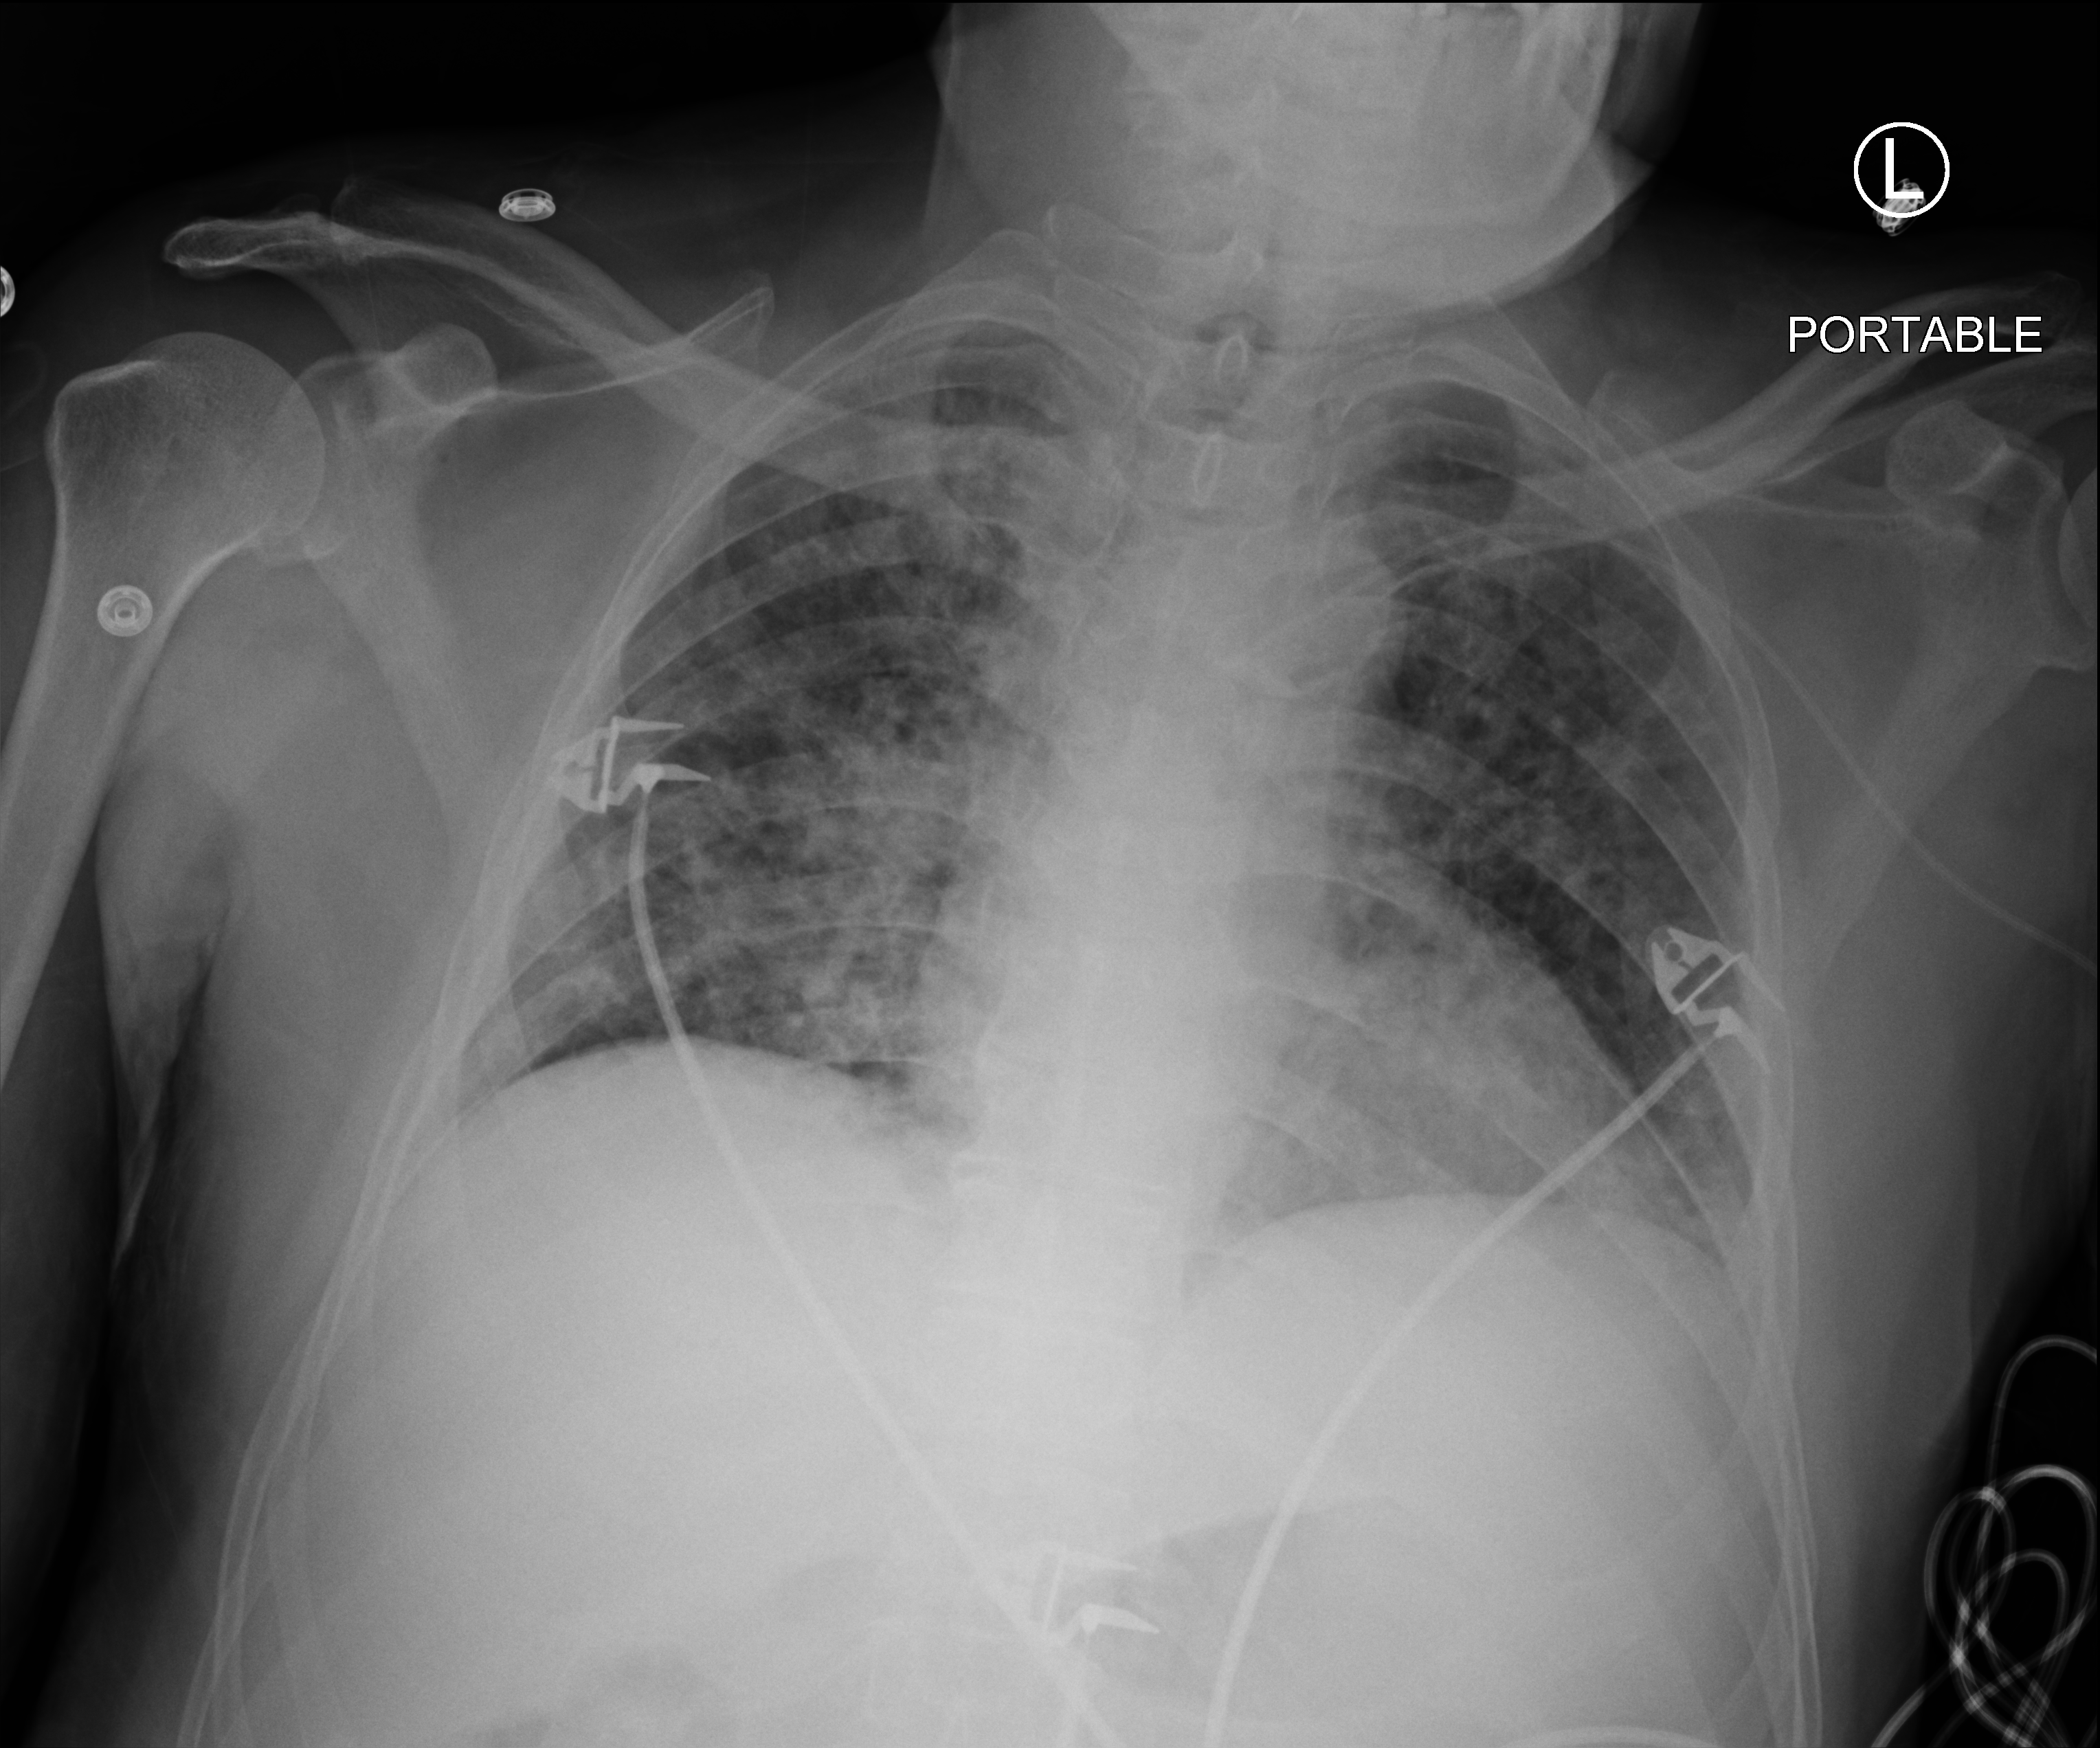
Portable chest radiograph, anteroposterior (AP) projection. Male patient hospitalised with COVID-19, age 18–59 years.
From the hospital-stay record, not from the radiograph (when in the stay this image was taken is not recorded):
- mechanically ventilated during this hospital stay: yes